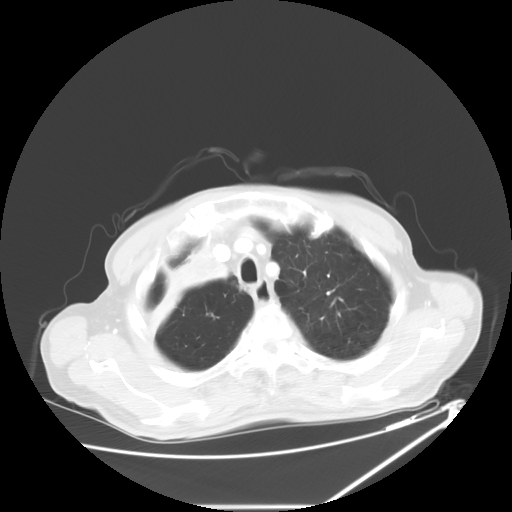
Chest CT, one axial slice. Position 51 of 60 along the scan axis. 120 kVp. Lung window (W 1500 / L -600 HU). 5 mm slice thickness. 512 × 512 image matrix, field of view 410 × 410 mm. Male patient, age 73 years. From the clinical record (not read from this slice): clinical TNM (as recorded): T2a N1 M0.
Annotated regions visible in this slice (rectangle marked by the reading radiologist):
- lung tumour (recorded histology: squamous cell carcinoma): box from (x=145, y=244) to (x=241, y=339) px